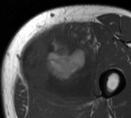
MRI of an extremity soft-tissue mass, one axial slice. Position 26 of 55 along the scan axis. MR volume resampled by the dataset authors to the PET/CT grid (not the native acquisition matrix). 3.27 mm slice thickness. 131 × 118 image matrix, field of view 128 × 115 mm. Male patient. Case-level facts recorded for this patient, not image findings: histological type: pleiomorphic liposarcoma; grade: high; site of the primary tumour: left thigh.
Outlined on this slice (expert contour drawn on MRI and transferred to this co-registered scan by the dataset authors):
- gross tumour volume including surrounding oedema: bounding box [x1, y1, x2, y2] px = [18, 23, 104, 104]
- gross tumour volume (mass): [20, 23, 97, 102]